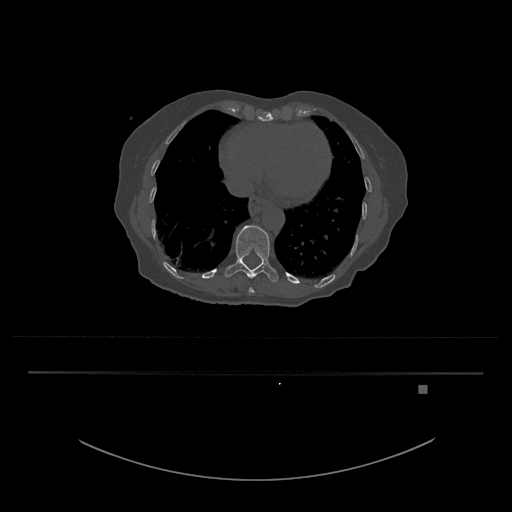
CT including the spine, one axial slice; reconstruction kernel Br40s/3; 120 kVp; bone window (W 1800 / L 400 HU); 512 × 512 image matrix, field of view 500 × 500 mm. Patient: female, 57 years. From the clinical record (not read from this slice): primary cancer: cervical.
Outlined on this slice (semi-automatic segmentation, software-assisted and operator-edited):
- T10 vertebra: box from (x=249, y=288) to (x=255, y=293) px
- T11 vertebra: (x=224, y=225)–(x=279, y=282)